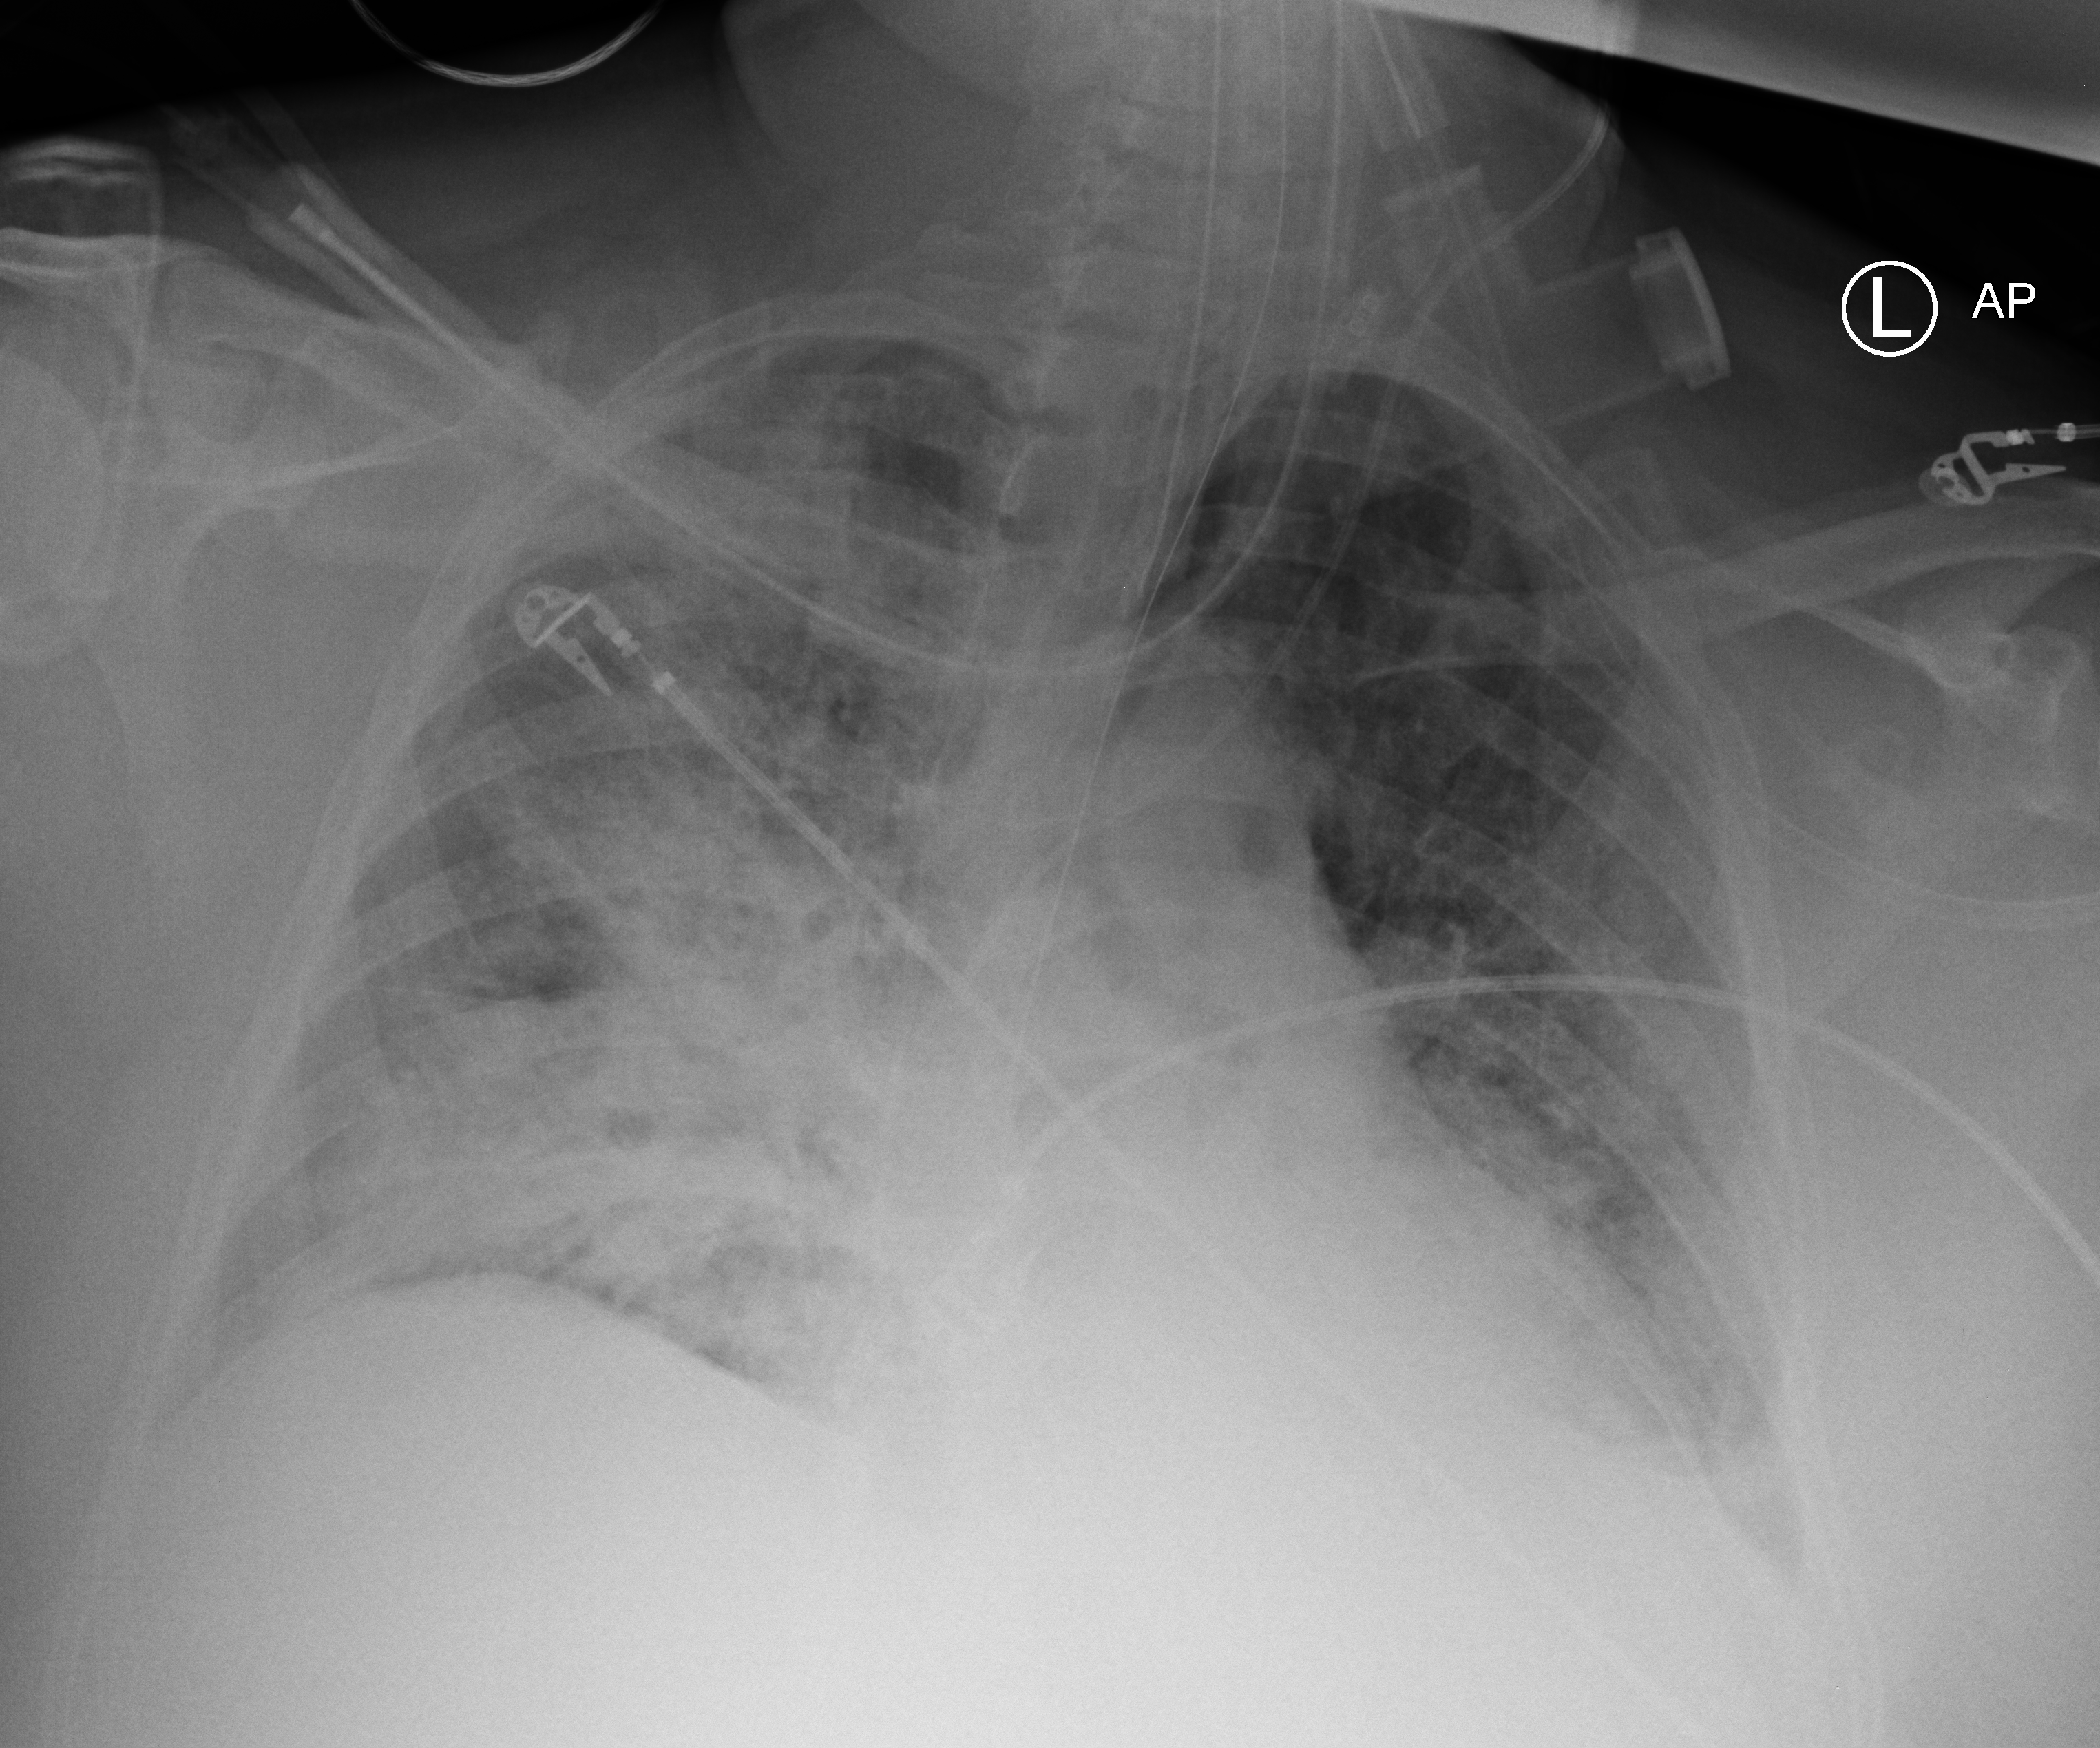
Portable chest radiograph; anteroposterior (AP) projection. Adult patient hospitalised with COVID-19, age 18–59 years.
Admission-level facts for this patient (not findings on this image; timing relative to this image not recorded):
- hypertension (admission record): no